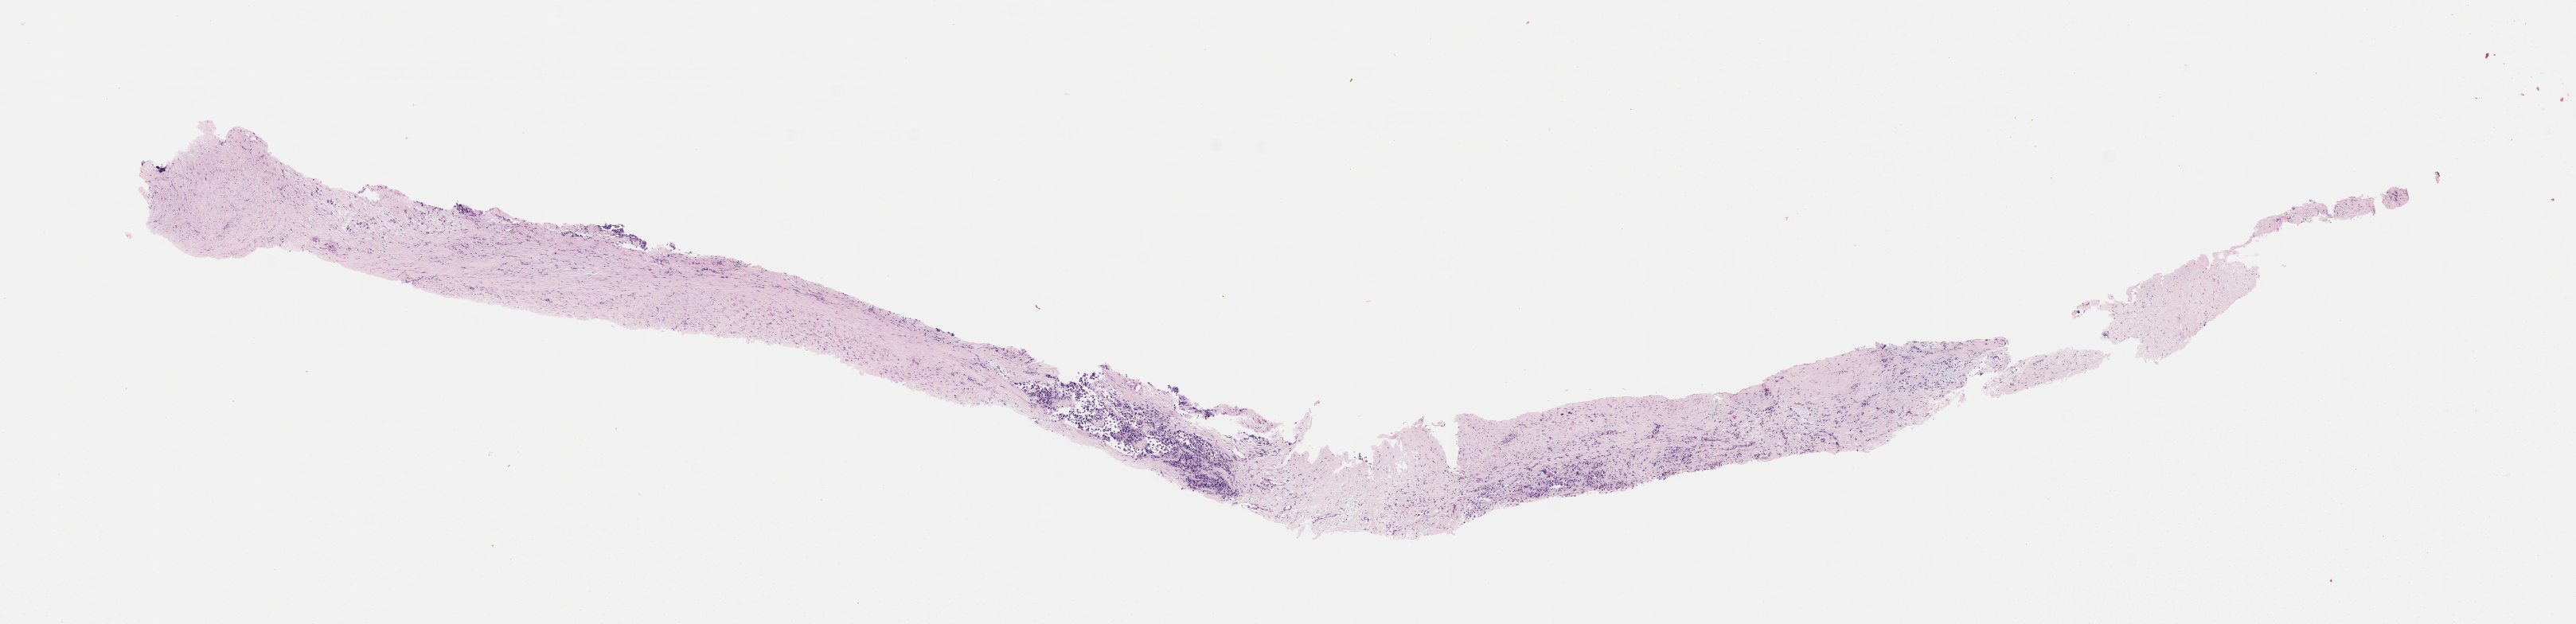
Haematoxylin and eosin whole-slide image of tumor tissue — whole scanned area (about 13.1 x 3.2 mm) shown as a low-resolution overview. Formalin-fixed, paraffin-embedded (FFPE) tissue. Site: right forearm. Patient: male, age 7.0 years at diagnosis.
Stage (as recorded): 4. Diagnosis: rhabdomyosarcoma; histological classification: rhabdomyosarcoma nos. Metastatic status at presentation (as recorded): metastatic (confirmed).